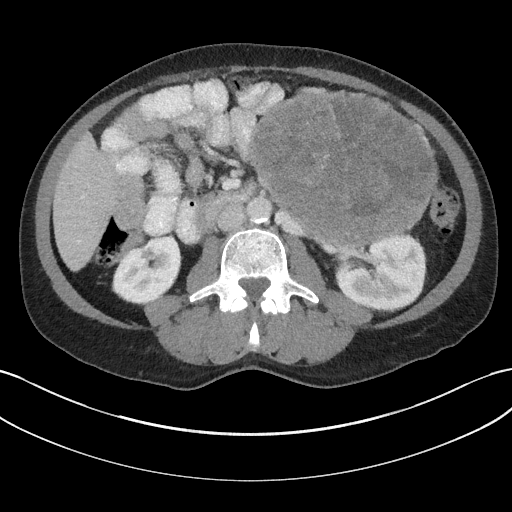
Contrast-enhanced abdominal CT, one axial slice; position 86 of 147 along the scan axis; 100 kVp; intravenous contrast given; soft-tissue window (W 400 / L 40 HU); 3 mm slice thickness; 512 × 512 image matrix, field of view 384 × 384 mm. Male patient, age 58 years. Case-level facts recorded for this patient, not image findings: diagnosis: adrenocortical carcinoma; tumour side: left adrenal; tumour size at pathology: 22 cm; Ki-67 index: 26 %; stage (as recorded): 2.
Annotated regions visible in this slice (semi-automatically segmented with operator editing):
- mass: box from (x=250, y=95) to (x=434, y=244) px